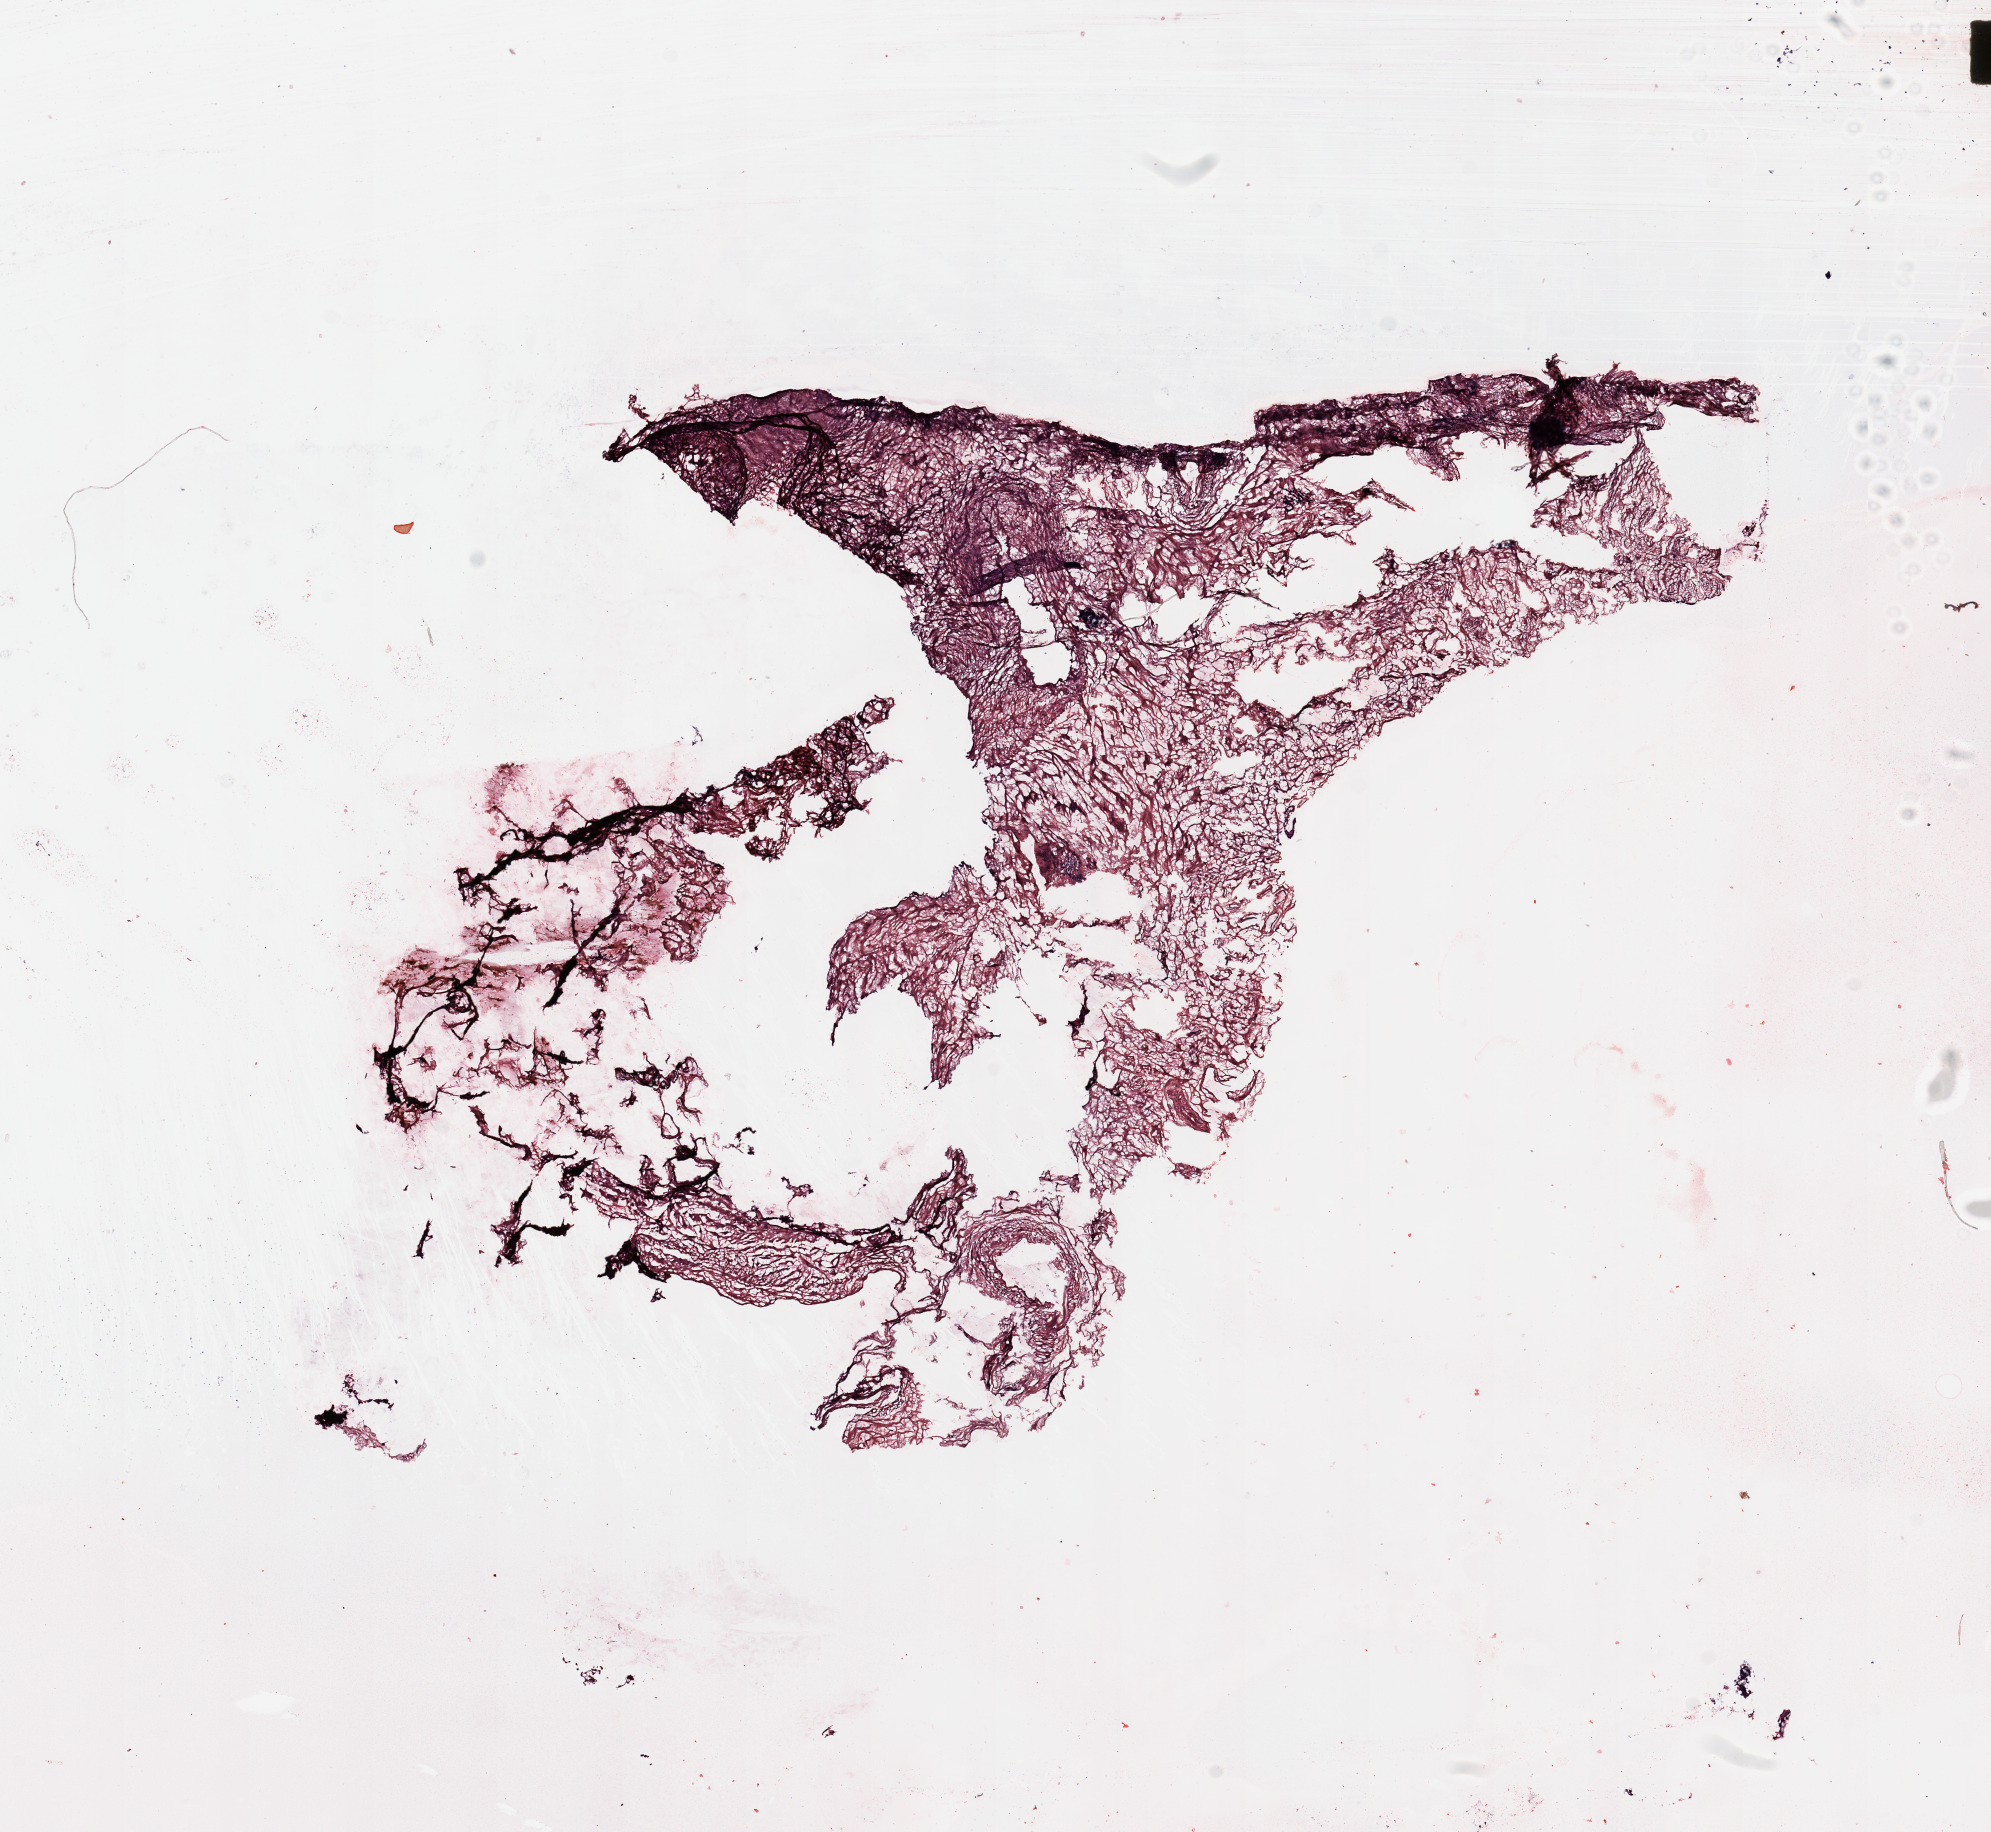
Digitized H&E-stained tissue section (whole slide), low-resolution overview of the scanned area, about 15.8 x 14.5 mm (from a 20x scan), uterus, normal (non-tumour) tissue. Patient: female, age 70 years.
* this section: normal (non-tumour) tissue from the same patient
* patient diagnosis: Endometrioid adenocarcinoma, NOS